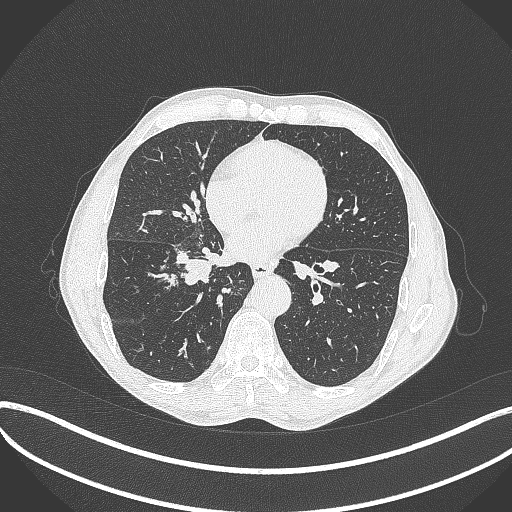
Chest CT, one axial slice. Position 186 of 481 along the scan axis. Lung window (W 1500 / L -600 HU). 1 mm slice thickness. 512 × 512 image matrix, field of view 400 × 400 mm. Patient: male, 65 years. Case-level facts recorded for this patient, not image findings: clinical TNM (as recorded): T2a N0 M0; histopathological grade: G2.
Structures marked on this image (rectangle marked by the reading radiologist):
- lung tumour (recorded histology: squamous cell carcinoma): box from (x=165, y=246) to (x=222, y=292) px